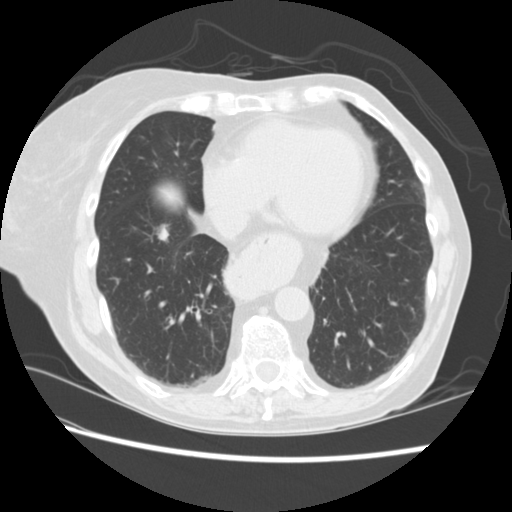
Low-dose screening chest CT, one axial slice. Slice 68 of 224 in the series (ordered by position). 120 kVp. Lung window (W 1500 / L -600 HU). 512 × 512 image matrix, field of view 340 × 340 mm.
Annotated regions visible in this slice (expert manual segmentation):
- lesion 2 (tumor, lower lobe of right lung): bounding box (x1, y1, x2, y2) in pixels: (158, 227, 169, 241)